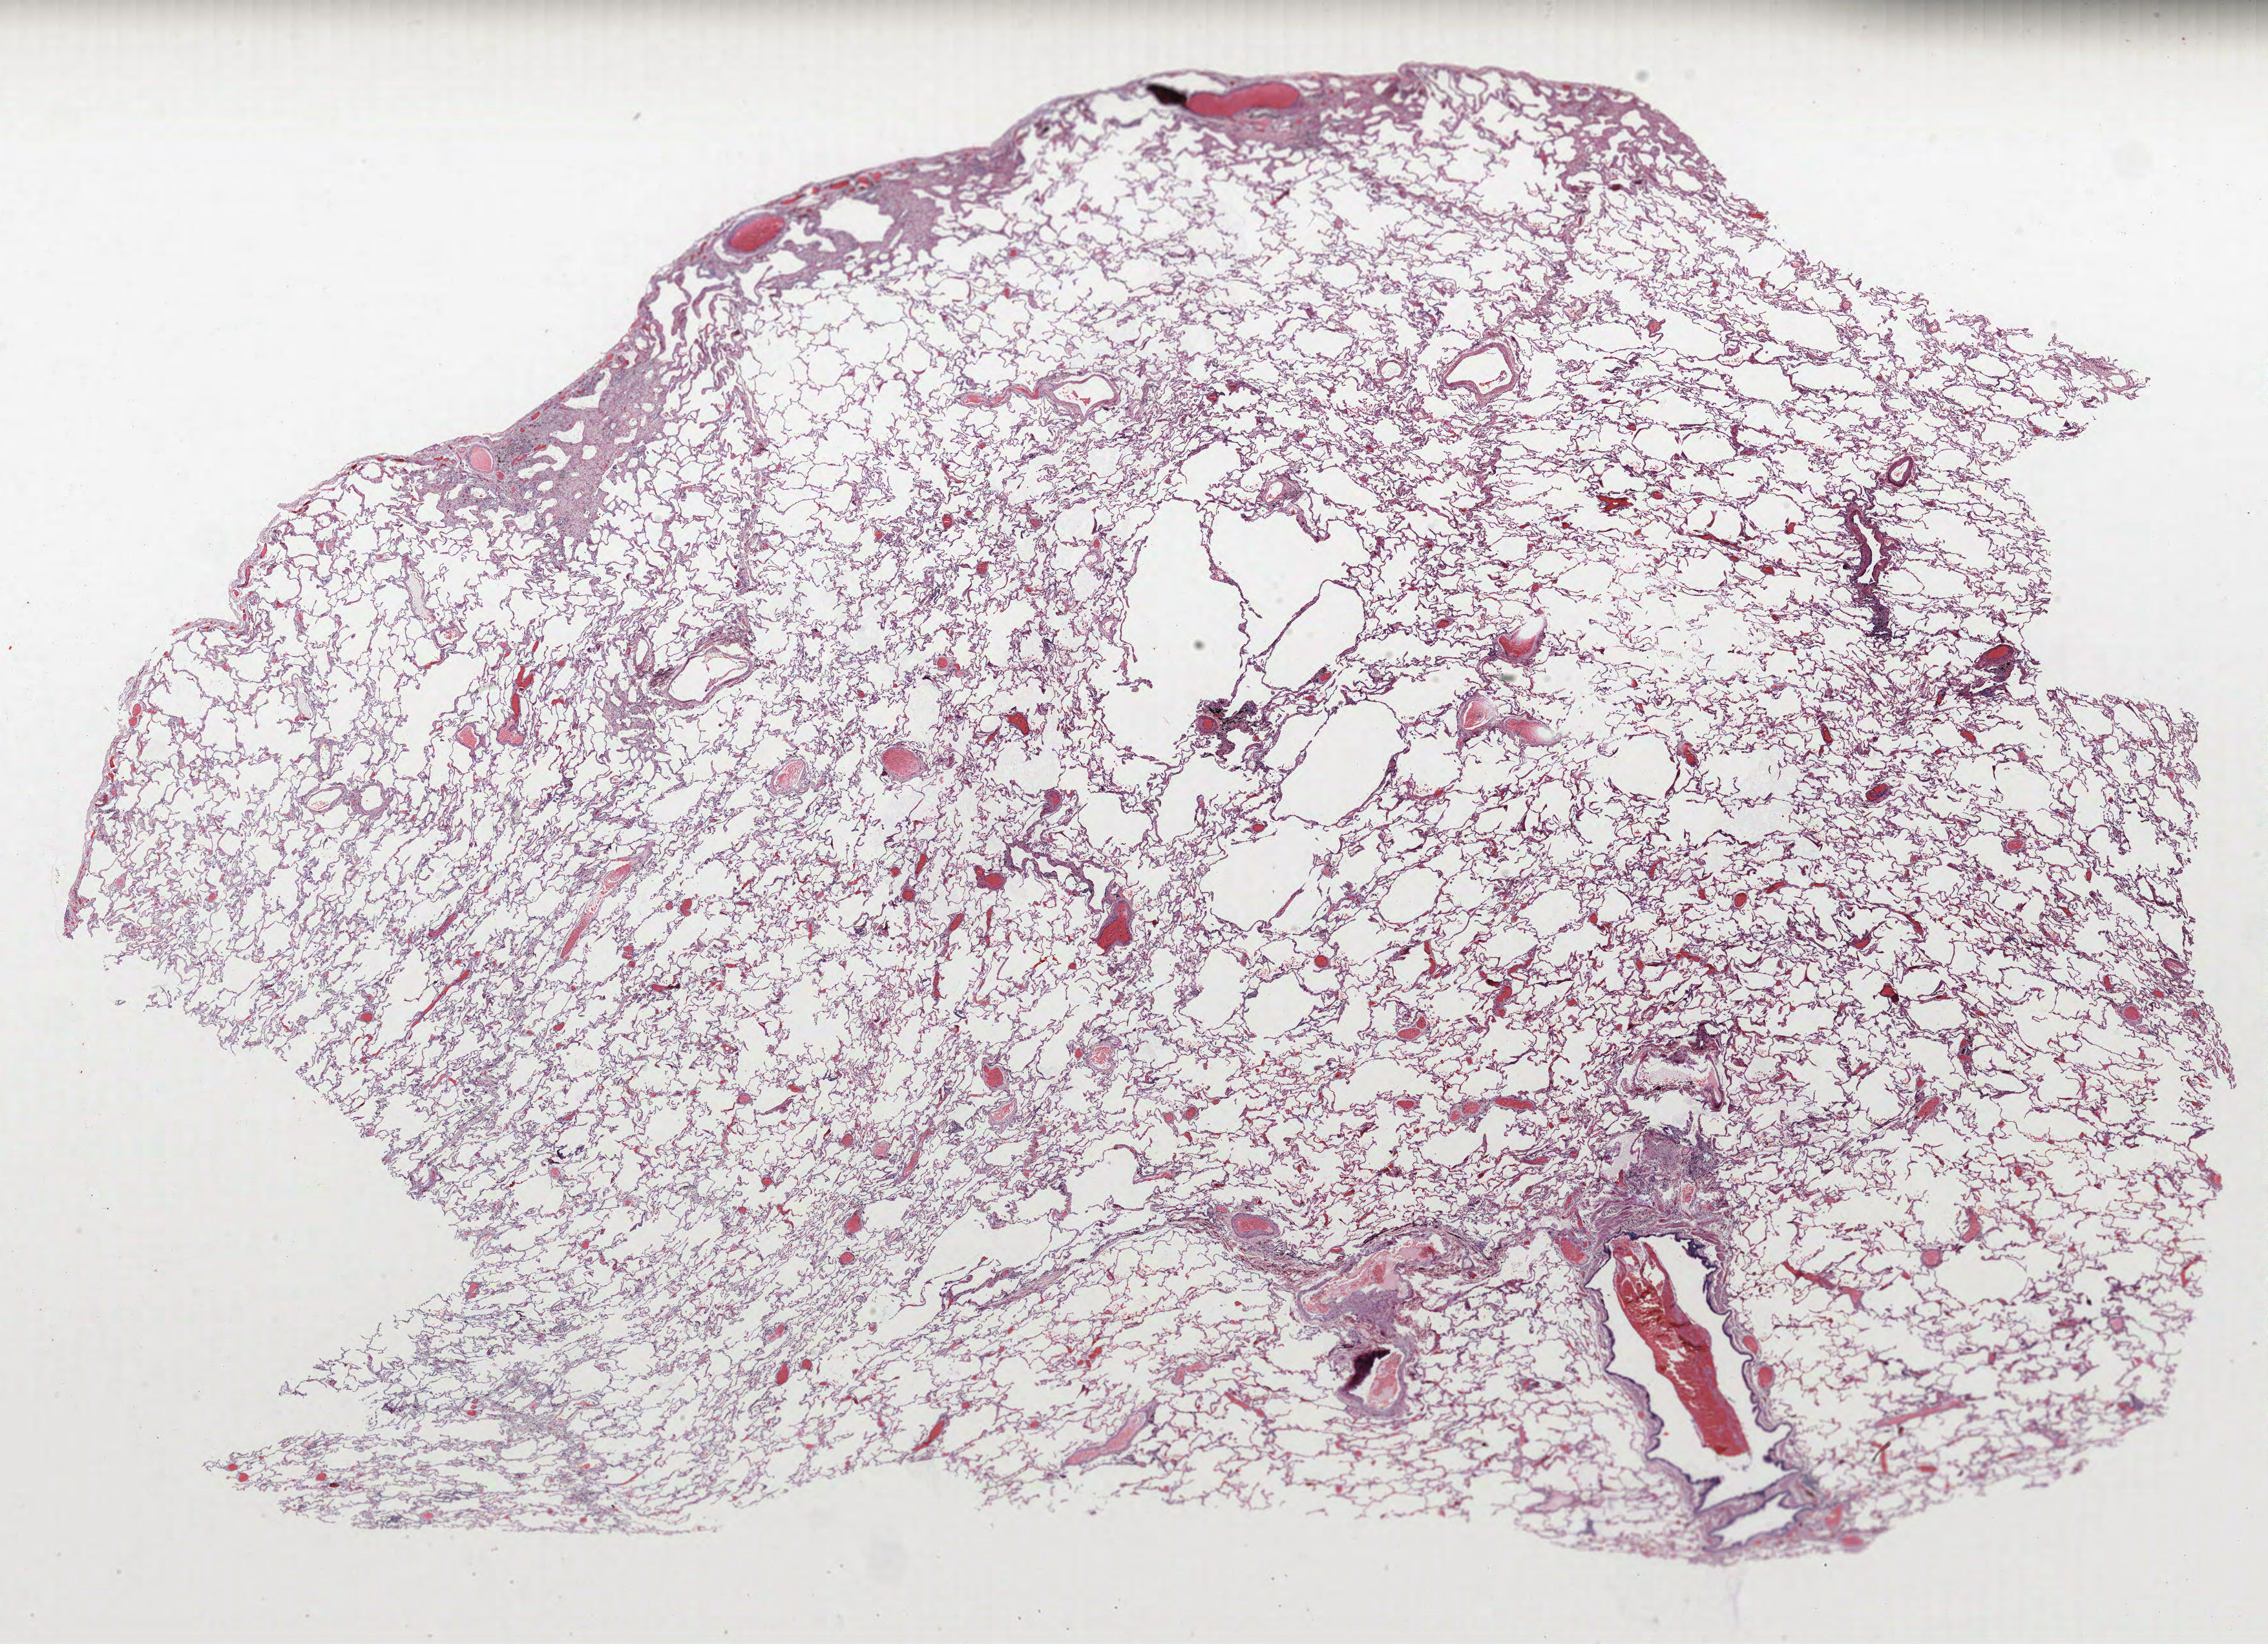
Hematoxylin and eosin (H&E) stained whole-slide image, whole scanned area (about 28.1 x 20.4 mm, slide scanned at 40x) shown as a low-resolution overview. Formalin-fixed paraffin-embedded (FFPE) section. Lung. Female, age 62 at enrolment. Former smoker at enrolment.
Participant's lung-cancer diagnosis: Squamous cell carcinoma, NOS.